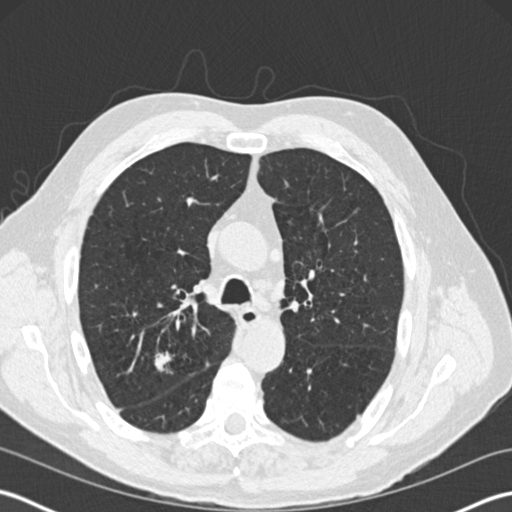
Chest CT (low-dose screening protocol), one axial image; third screening round (two years after baseline); lung window (W 1500 / L -600 HU); 2 mm slice thickness; standard (soft-tissue) reconstruction kernel (B30f); slice 71 of 199 in the series. Male participant, aged 65 years at enrolment. Former smoker at enrolment.
• Lesion marked by an expert reader, bounding box [x1, y1, x2, y2] px = [141, 348, 181, 383].
• The screening reader recorded 6 non-calcified nodules or masses ≥4 mm on this exam; which of them this box marks is not recorded.
• Lung cancer was diagnosed 78 days after this screen: adenocarcinoma, NOS, right upper lobe, moderately differentiated (G2), stage IA (AJCC 6th edition), 16 mm at pathology.